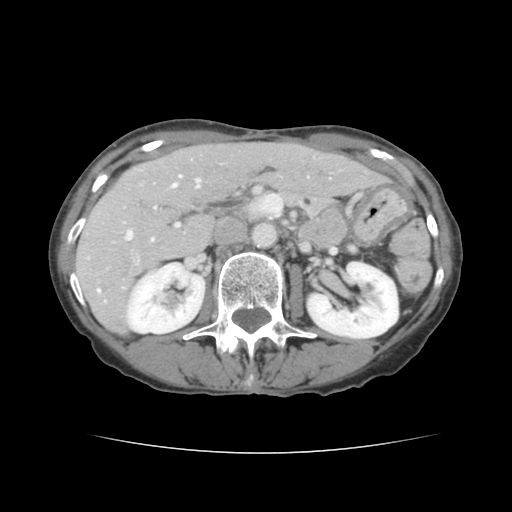
Contrast-enhanced abdominal CT, one axial slice. Position 69 of 136 along the scan axis. 120 kVp. Soft-tissue window (W 400 / L 40 HU). 2.5 mm slice thickness. 512 × 512 image matrix, field of view 319 × 319 mm. Female patient, age 77 years. Case-level facts recorded for this patient, not image findings: diagnosis: colorectal cancer liver metastases, imaged before liver resection; multiple liver metastases: yes; largest metastasis: 3 cm; disease in both lobes: no.
Annotated regions visible in this slice (manually delineated by an expert):
- hepatic veins: bounding box [x1, y1, x2, y2] px = [126, 175, 200, 239]
- liver: [77, 143, 383, 333]
- planned liver remnant (the part of the liver to remain after resection): [158, 143, 383, 203]
- portal vein (with intrahepatic branches): [98, 206, 179, 292]